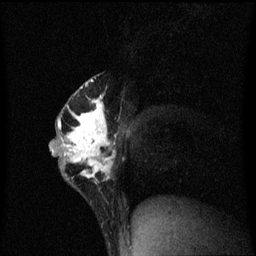
Breast MRI (dynamic contrast-enhanced), one sagittal slice; slice 36 of 60 in the series (ordered by position); dynamic contrast-enhanced series, image 2 of 3 at this slice position (ordered by acquisition); 1.5 T; TE 4.2 ms, TR 8.4 ms; 2 mm slice thickness; 256 × 256 image matrix, field of view 200 × 200 mm. Patient: female, 40 years.
Structures marked on this image (semi-automatic segmentation, software-assisted and operator-edited):
- analysis volume of interest (the breast-tissue region the enhancement analysis was run in; not a lesion): box from (x=51, y=74) to (x=116, y=199) px
- tumour enhancement mask (voxels above the 70 % enhancement threshold inside the analysis volume of interest): (x=51, y=80)–(x=116, y=185)